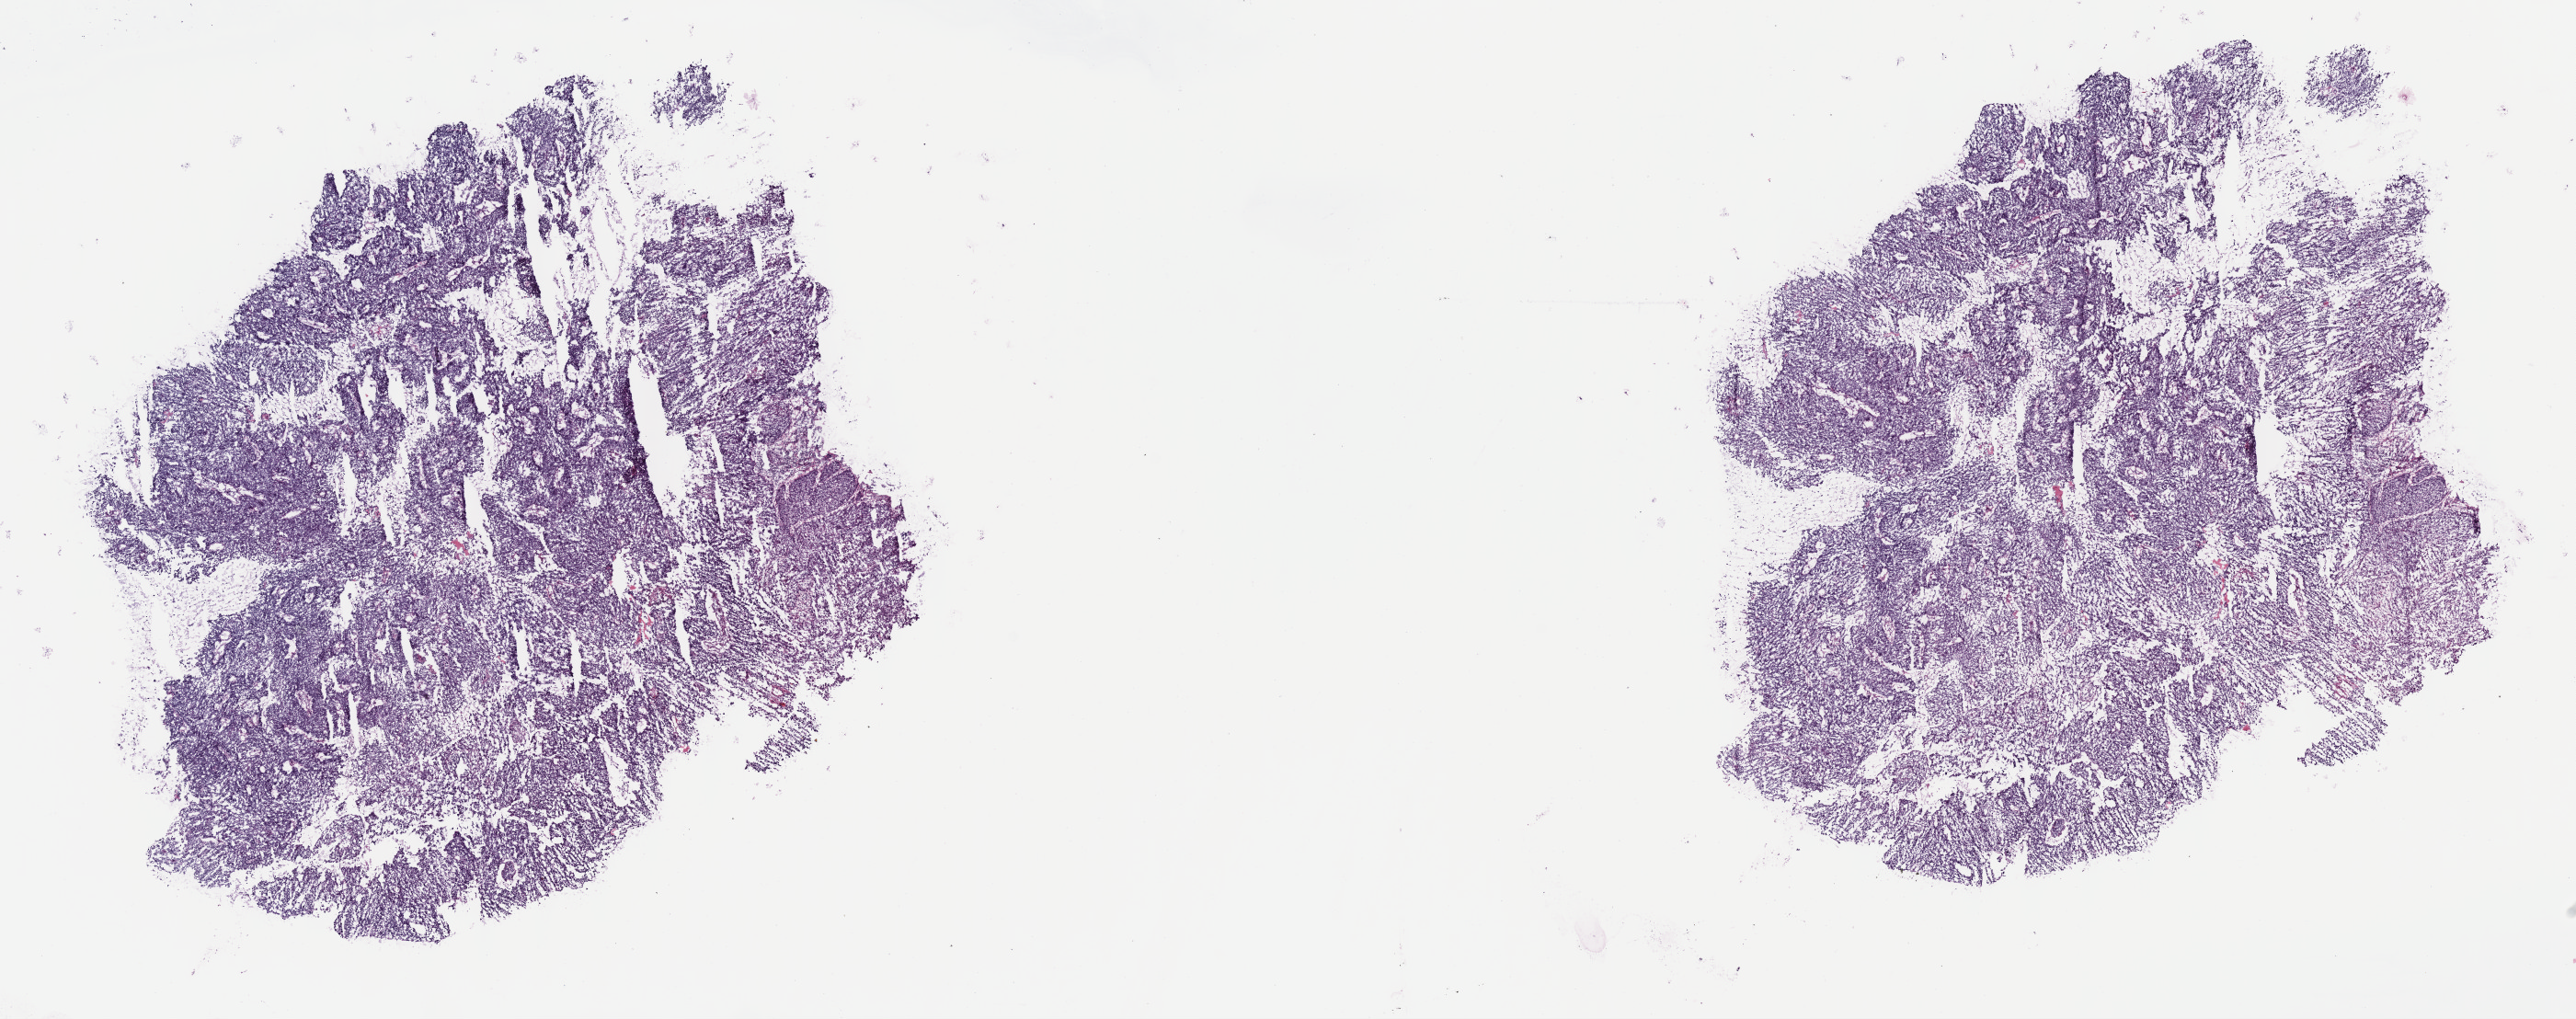
Digitized Hematoxylin and eosin (H&E) stained tissue section (whole slide) — a low-resolution overview of the entire scanned area, about 22.7 x 9.0 mm. Frozen section from the top of the tissue portion. Primary tumour sample from the cervix. Female, age 64 years at initial diagnosis. Histologic grade: G3 (poorly differentiated). Slide review estimates, as recorded: tumour cells 85%, tumour nuclei 90%, normal cells 0%, stromal cells 15%, necrosis 0%. Infiltration values recorded for this section: lymphocyte infiltration 0%, monocyte infiltration 0%, neutrophil infiltration 0%.
FIGO stage: IB1. Diagnosis: Squamous cell carcinoma, NOS (cervix uteri).